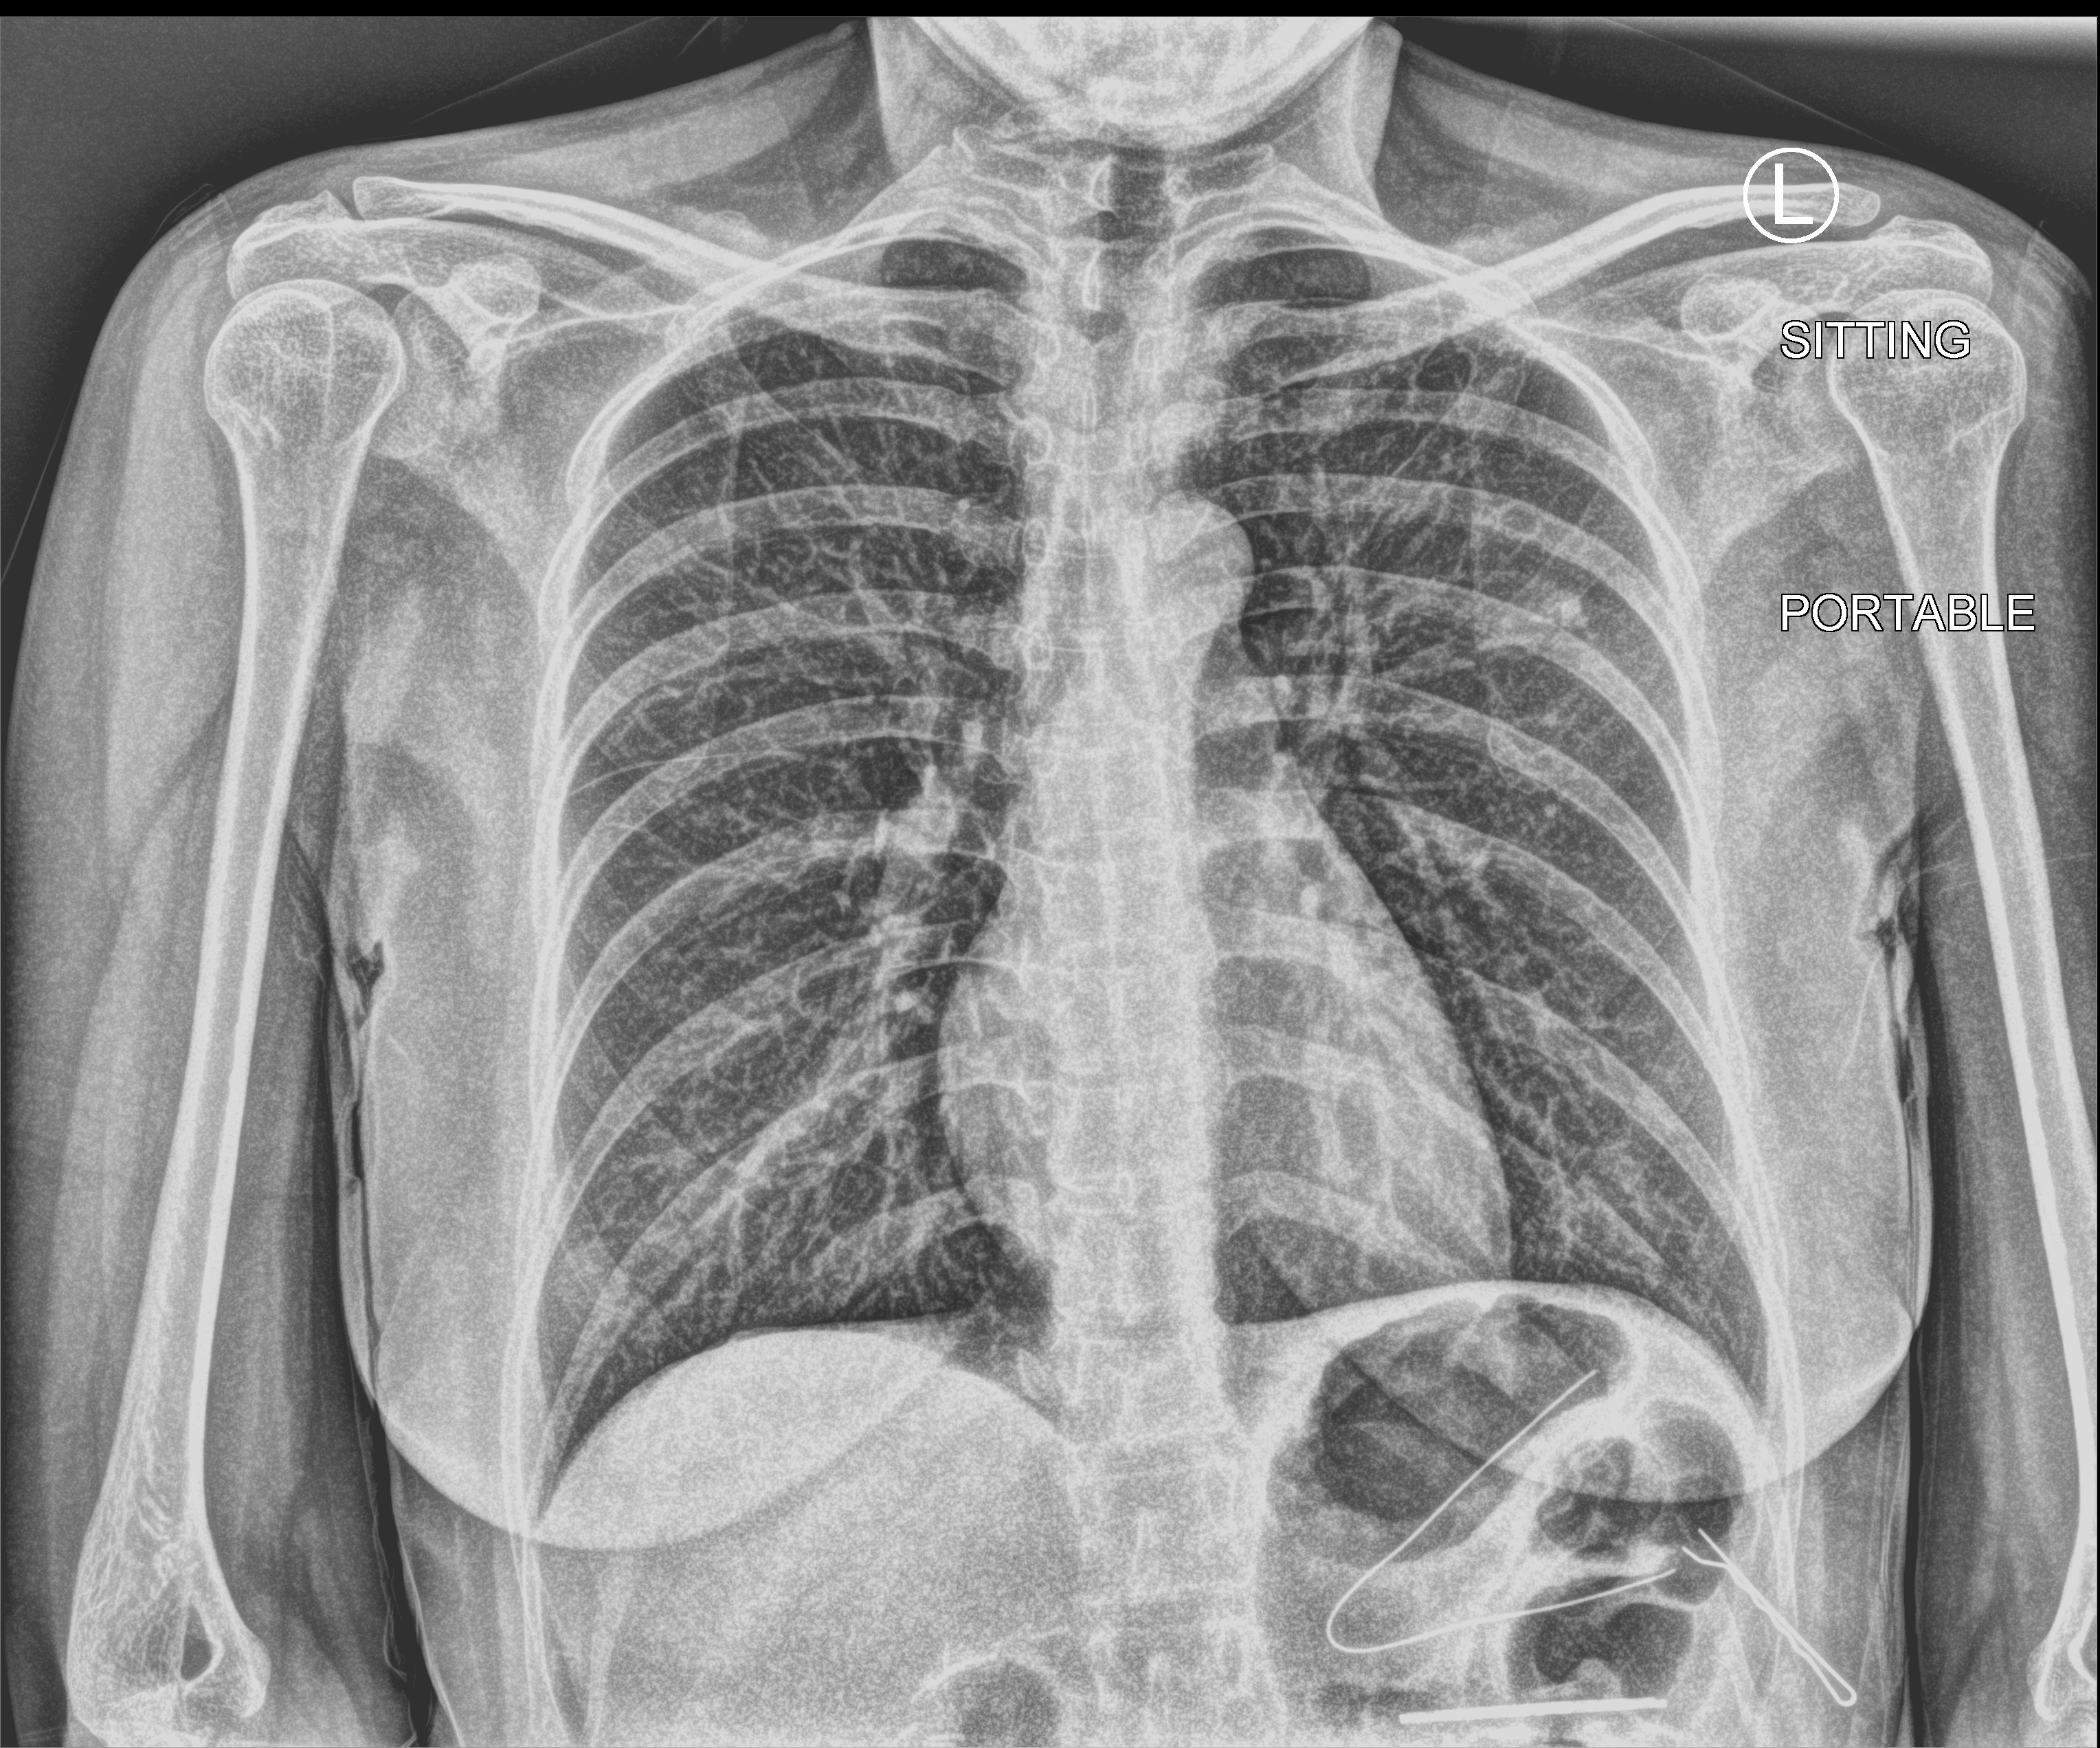
Chest X-ray (portable); anteroposterior (AP) projection. Female patient hospitalised with COVID-19, age 18–59 years.
Admission-level facts for this patient (not findings on this image; timing relative to this image not recorded): COPD (admission record): no; mechanically ventilated during this hospital stay: no; admitted to intensive care during this hospital stay: no.